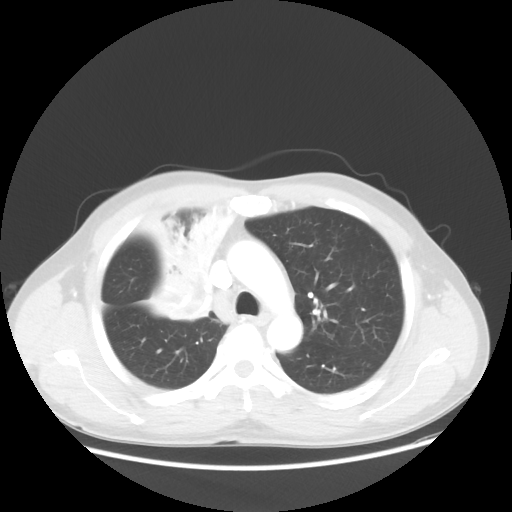
Chest CT, one axial slice. Position 38 of 56 along the scan axis. Reconstruction kernel STANDARD. 100 kVp. Lung window (W 1500 / L -600 HU). 5 mm slice thickness. 512 × 512 image matrix, field of view 398 × 398 mm. Patient: male, 60 years. From the clinical record (not read from this slice): clinical TNM (as recorded): T2a N1 M0.
Outlined on this slice (rectangle marked by the reading radiologist):
- lung tumour (recorded histology: squamous cell carcinoma): bounding box [x1, y1, x2, y2] px = [117, 192, 236, 330]